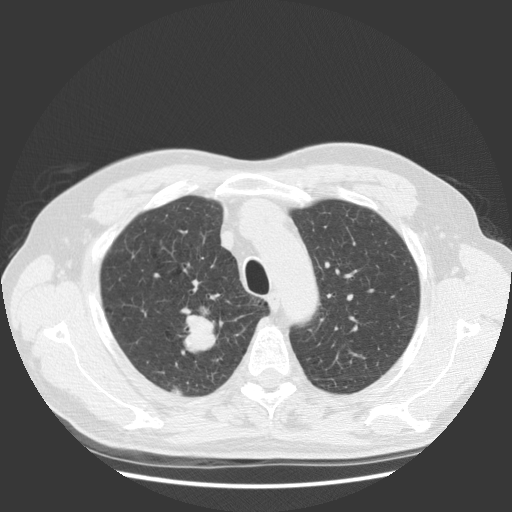
Low-dose screening chest CT, one axial slice. Position 99 of 131 along the scan axis. Reconstruction kernel STANDARD. Lung window (W 1500 / L -600 HU). 2.5 mm slice thickness. 512 × 512 image matrix, field of view 369 × 369 mm.
Outlined on this slice (manually delineated by an expert):
- lesion 1 (tumor, upper lobe of right lung): bounding box [x1, y1, x2, y2] px = [184, 314, 216, 353]
- lesion 2 (tumor, upper lobe of right lung): [173, 389, 181, 394]